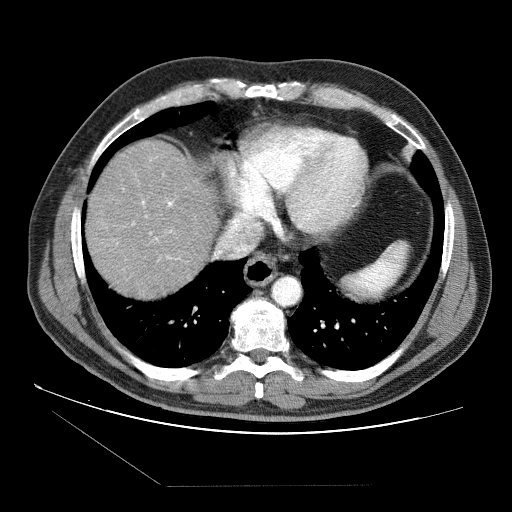
Contrast-enhanced abdominal CT (liver protocol), one axial slice. Position 74 of 87 along the scan axis. Reconstruction kernel STANDARD. Soft-tissue window (W 400 / L 40 HU). 512 × 512 image matrix, field of view 400 × 400 mm. Case-level facts recorded for this patient, not image findings: diagnosis: hepatocellular carcinoma (patient treated with transarterial chemoembolisation; whether this scan precedes or follows treatment is not stated here); TNM stage (as recorded): Stage-II.
Annotated regions visible in this slice (semi-automatically segmented with operator editing):
- liver parenchyma outside the tumour (the mass and vessels are separate outlines, so this box may not span the whole liver): bounding box (x1, y1, x2, y2) in pixels: (86, 140, 218, 298)
- liver vessels: (117, 189, 179, 261)